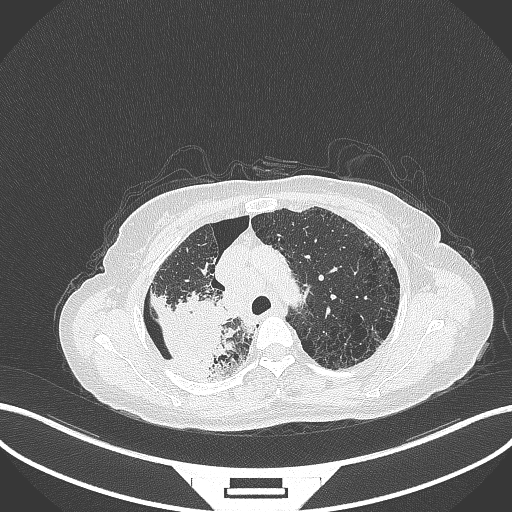
Chest CT, one axial slice. Slice 263 of 408 in the series (ordered by position). Reconstruction kernel B70f. Lung window (W 1500 / L -600 HU). 1 mm slice thickness. 512 × 512 image matrix, field of view 400 × 400 mm. Female patient, age 64 years. Case-level facts recorded for this patient, not image findings: clinical TNM (as recorded): T3 N3 M0.
Outlined on this slice (bounding box drawn by a radiologist):
- lung tumour (recorded histology: squamous cell carcinoma): bounding box <144,285,226,376> (left, top, right, bottom; pixels)